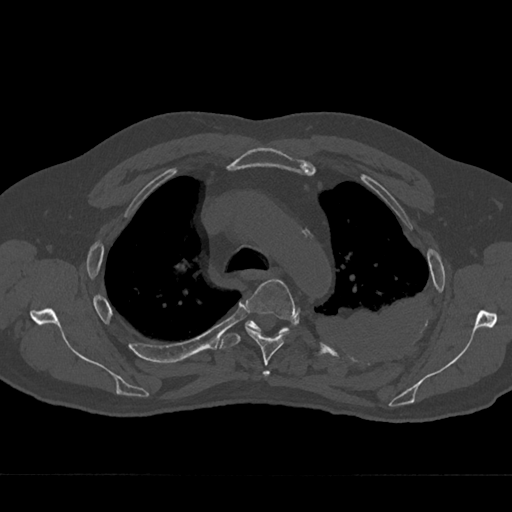
CT including the spine, one axial slice. Position 508 of 797 along the scan axis. Reconstruction kernel Br40s/3. 120 kVp. Bone window (W 1800 / L 400 HU). 0.5 mm slice thickness. 512 × 512 image matrix, field of view 377 × 377 mm. Patient: male, 75 years. Case-level facts recorded for this patient, not image findings: primary cancer: renal.
Annotated regions visible in this slice (semi-automatically segmented with operator editing):
- T3 vertebra: bounding box (x1, y1, x2, y2) in pixels: (263, 371, 270, 375)
- T4 vertebra: (245, 279, 295, 377)
- T5 vertebra: (220, 320, 288, 349)